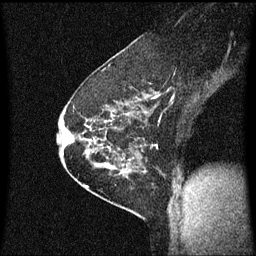
Breast MRI (dynamic contrast-enhanced), one sagittal slice; slice 41 of 60 in the series (ordered by position); dynamic contrast-enhanced series, image 2 of 3 at this slice position (ordered by acquisition); 1.5 T; TE 4.2 ms, TR 8.4 ms; 256 × 256 image matrix, field of view 200 × 200 mm. Female patient, age 60 years.
Structures marked on this image (semi-automatic segmentation, software-assisted and operator-edited):
- analysis volume of interest (the breast-tissue region the enhancement analysis was run in; not a lesion): bounding box <69,66,147,193> (left, top, right, bottom; pixels)
- tumour enhancement mask (voxels above the 70 % enhancement threshold inside the analysis volume of interest): <69,96,147,173>